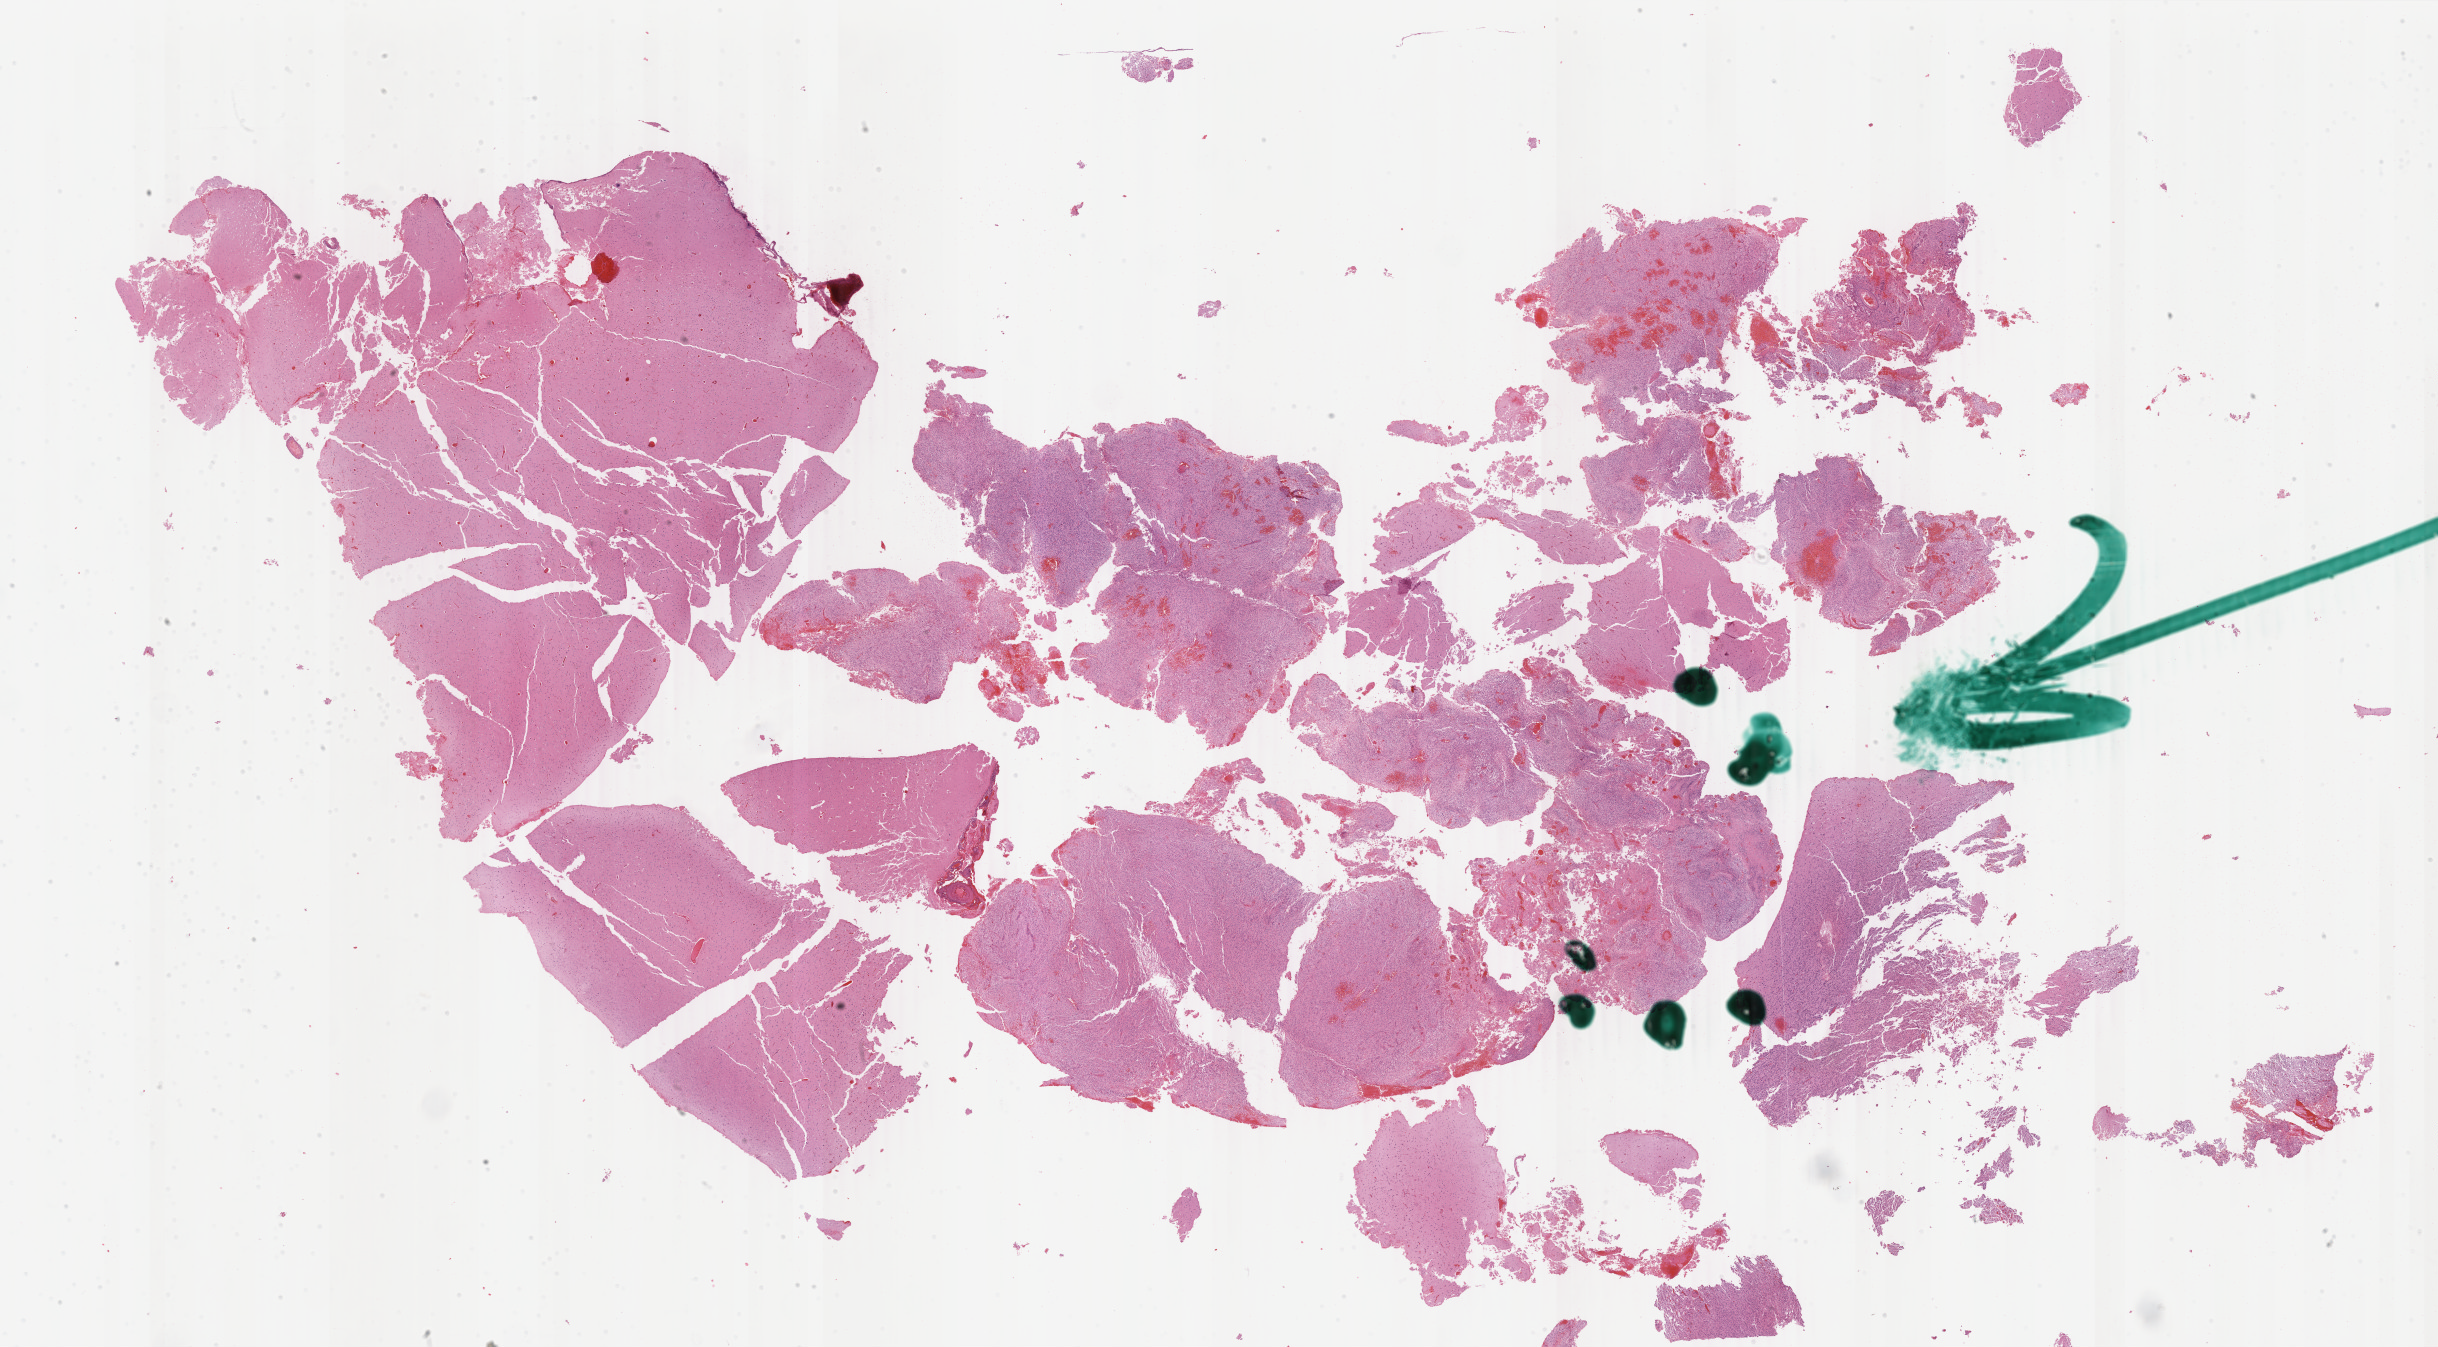
Hematoxylin and eosin (H&E) stained whole-slide image — a low-resolution overview of the entire scanned area, about 38.8 x 21.4 mm, formalin-fixed paraffin-embedded (FFPE) diagnostic section, primary tumour sample from the brain. Patient: male, age at initial diagnosis 48 years.
Diagnosis: Glioblastoma.